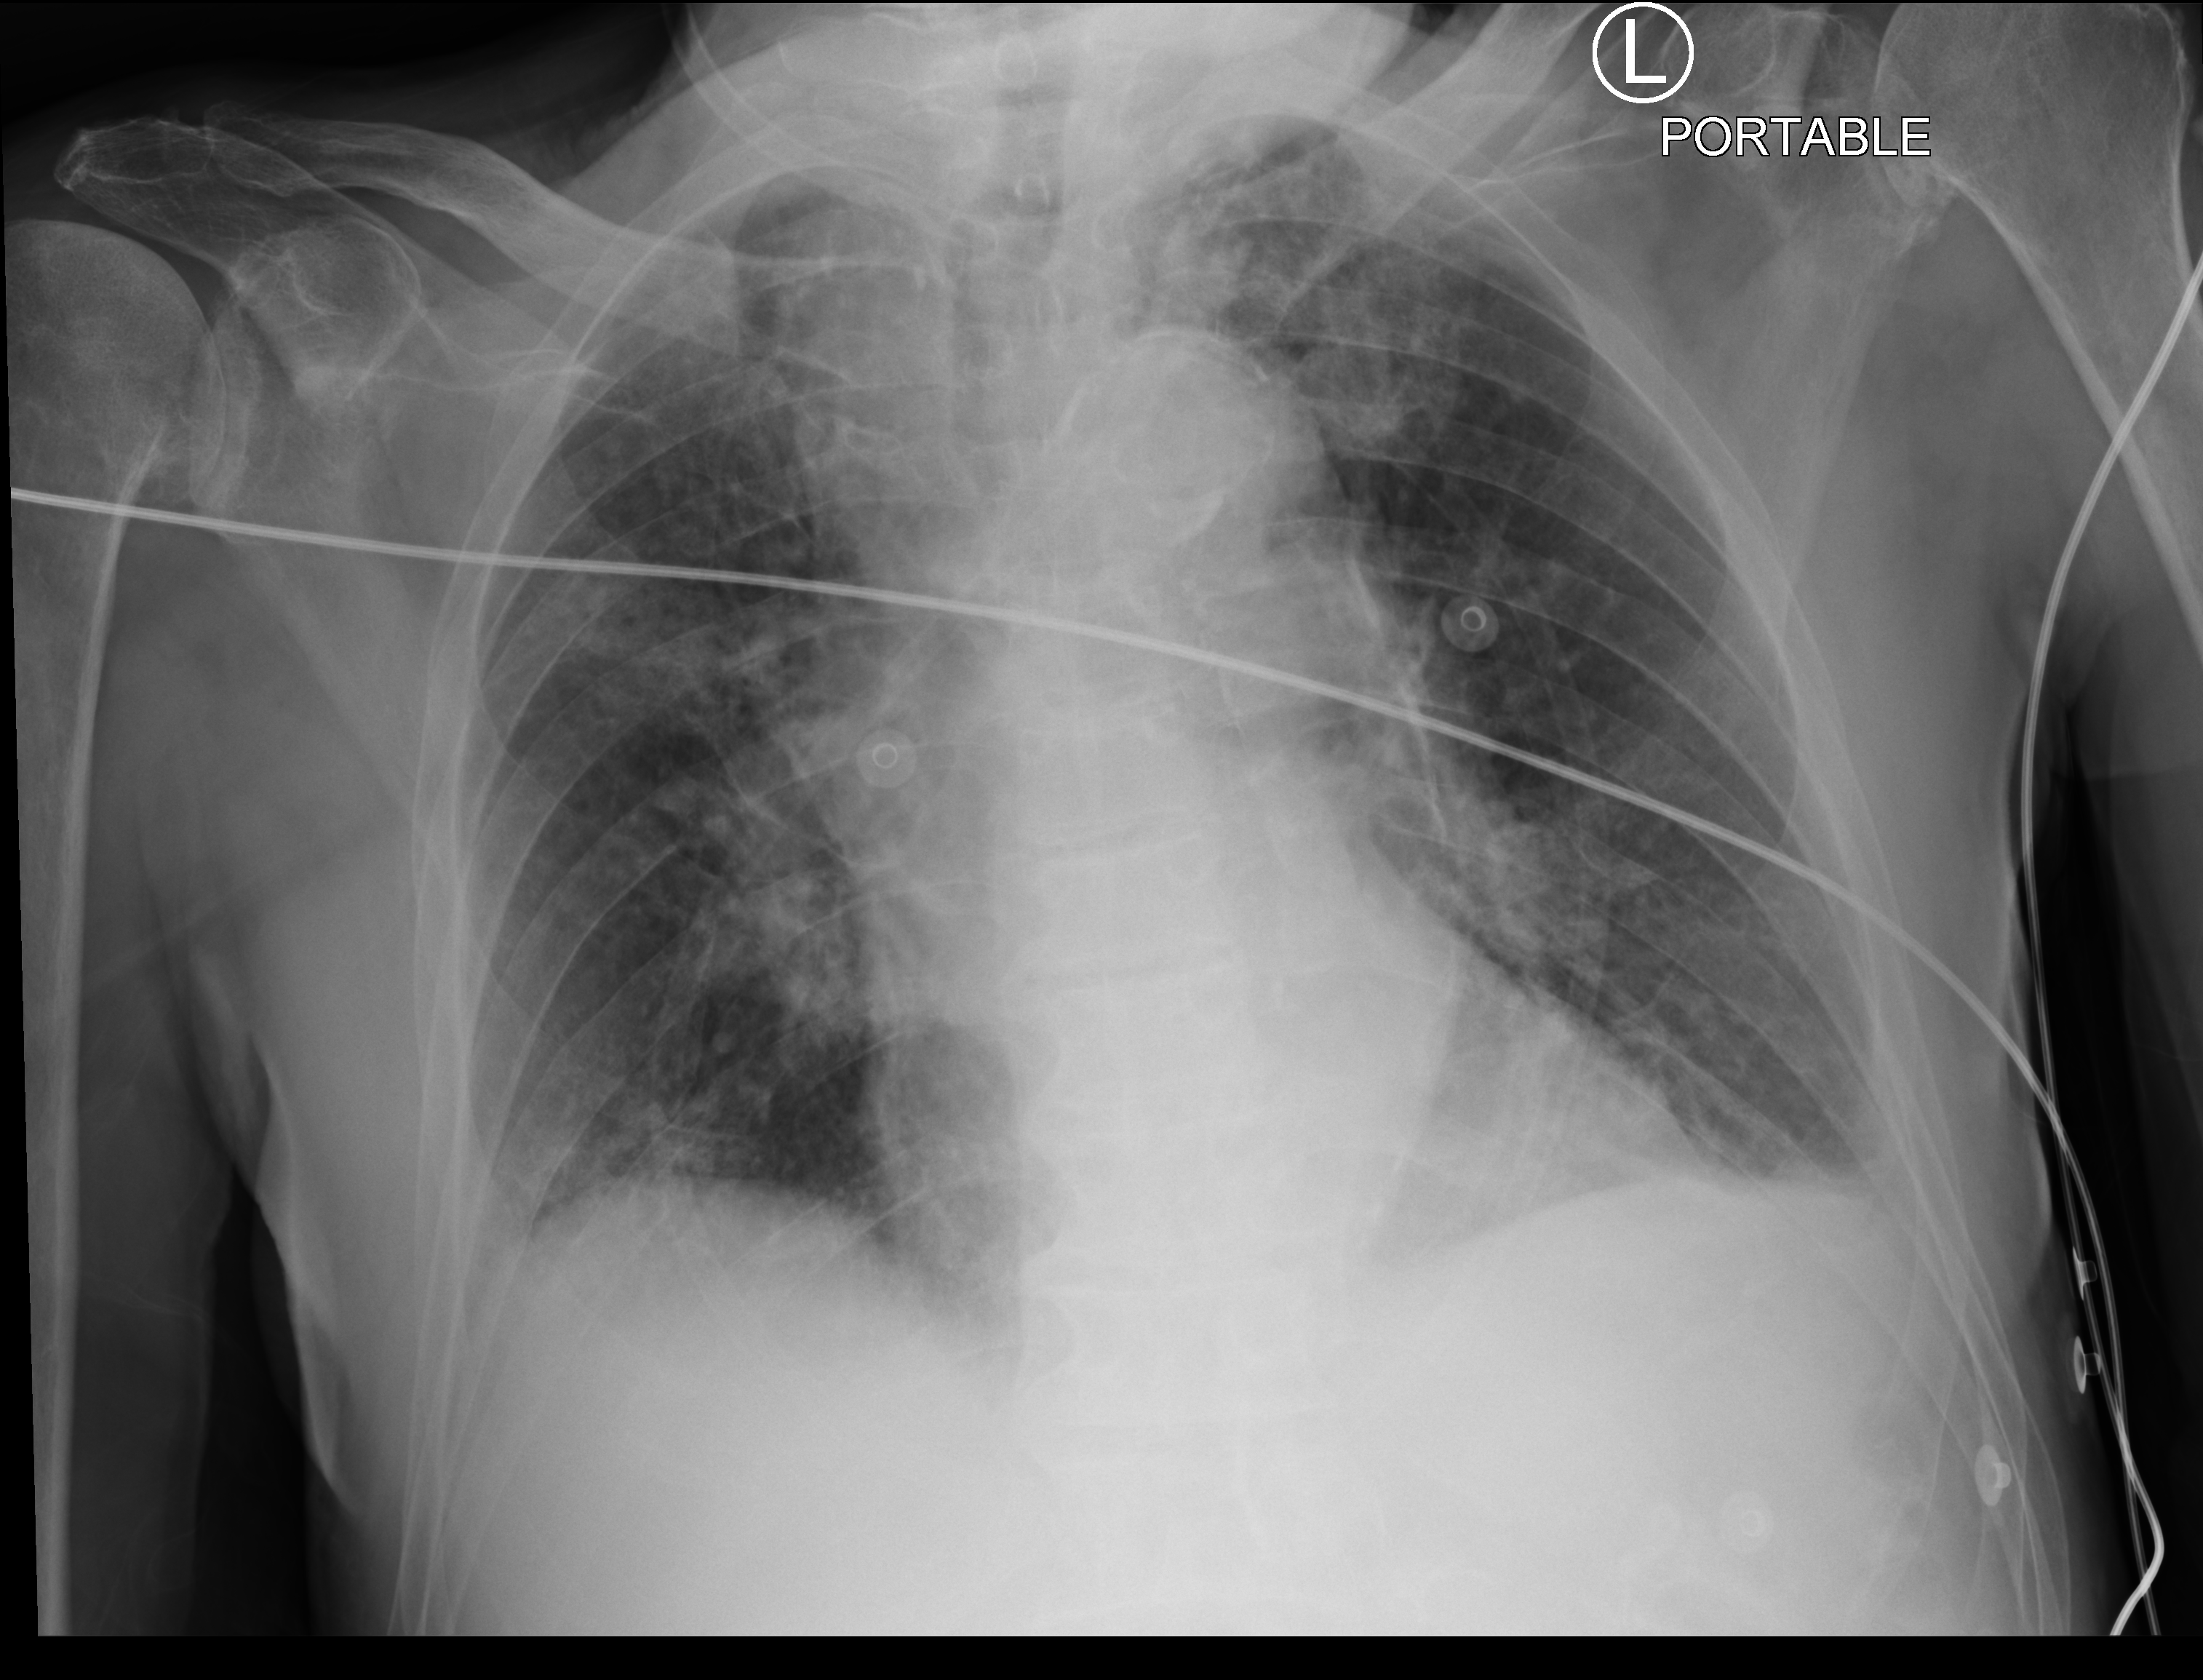
Chest X-ray (portable). Patient hospitalised with COVID-19; male, aged 75–90 years.
From the hospital-stay record, not from the radiograph (when in the stay this image was taken is not recorded): admitted to intensive care during this hospital stay: no; hypertension (admission record): yes.